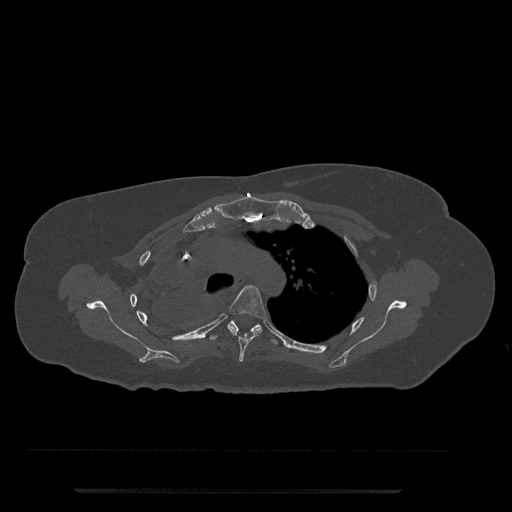
CT including the spine, one axial slice; position 573 of 797 along the scan axis; reconstruction kernel Br40s/3; bone window (W 1800 / L 400 HU); 0.5 mm slice thickness; 512 × 512 image matrix, field of view 440 × 440 mm. Patient: female, 51 years. From the clinical record (not read from this slice): primary cancer: neuro; vertebrae with lytic lesions (as recorded): T8.
Annotated regions visible in this slice (semi-automatic segmentation, software-assisted and operator-edited):
- T4 vertebra: bounding box <211,285,266,362> (left, top, right, bottom; pixels)
- T5 vertebra: <210,317,278,345>